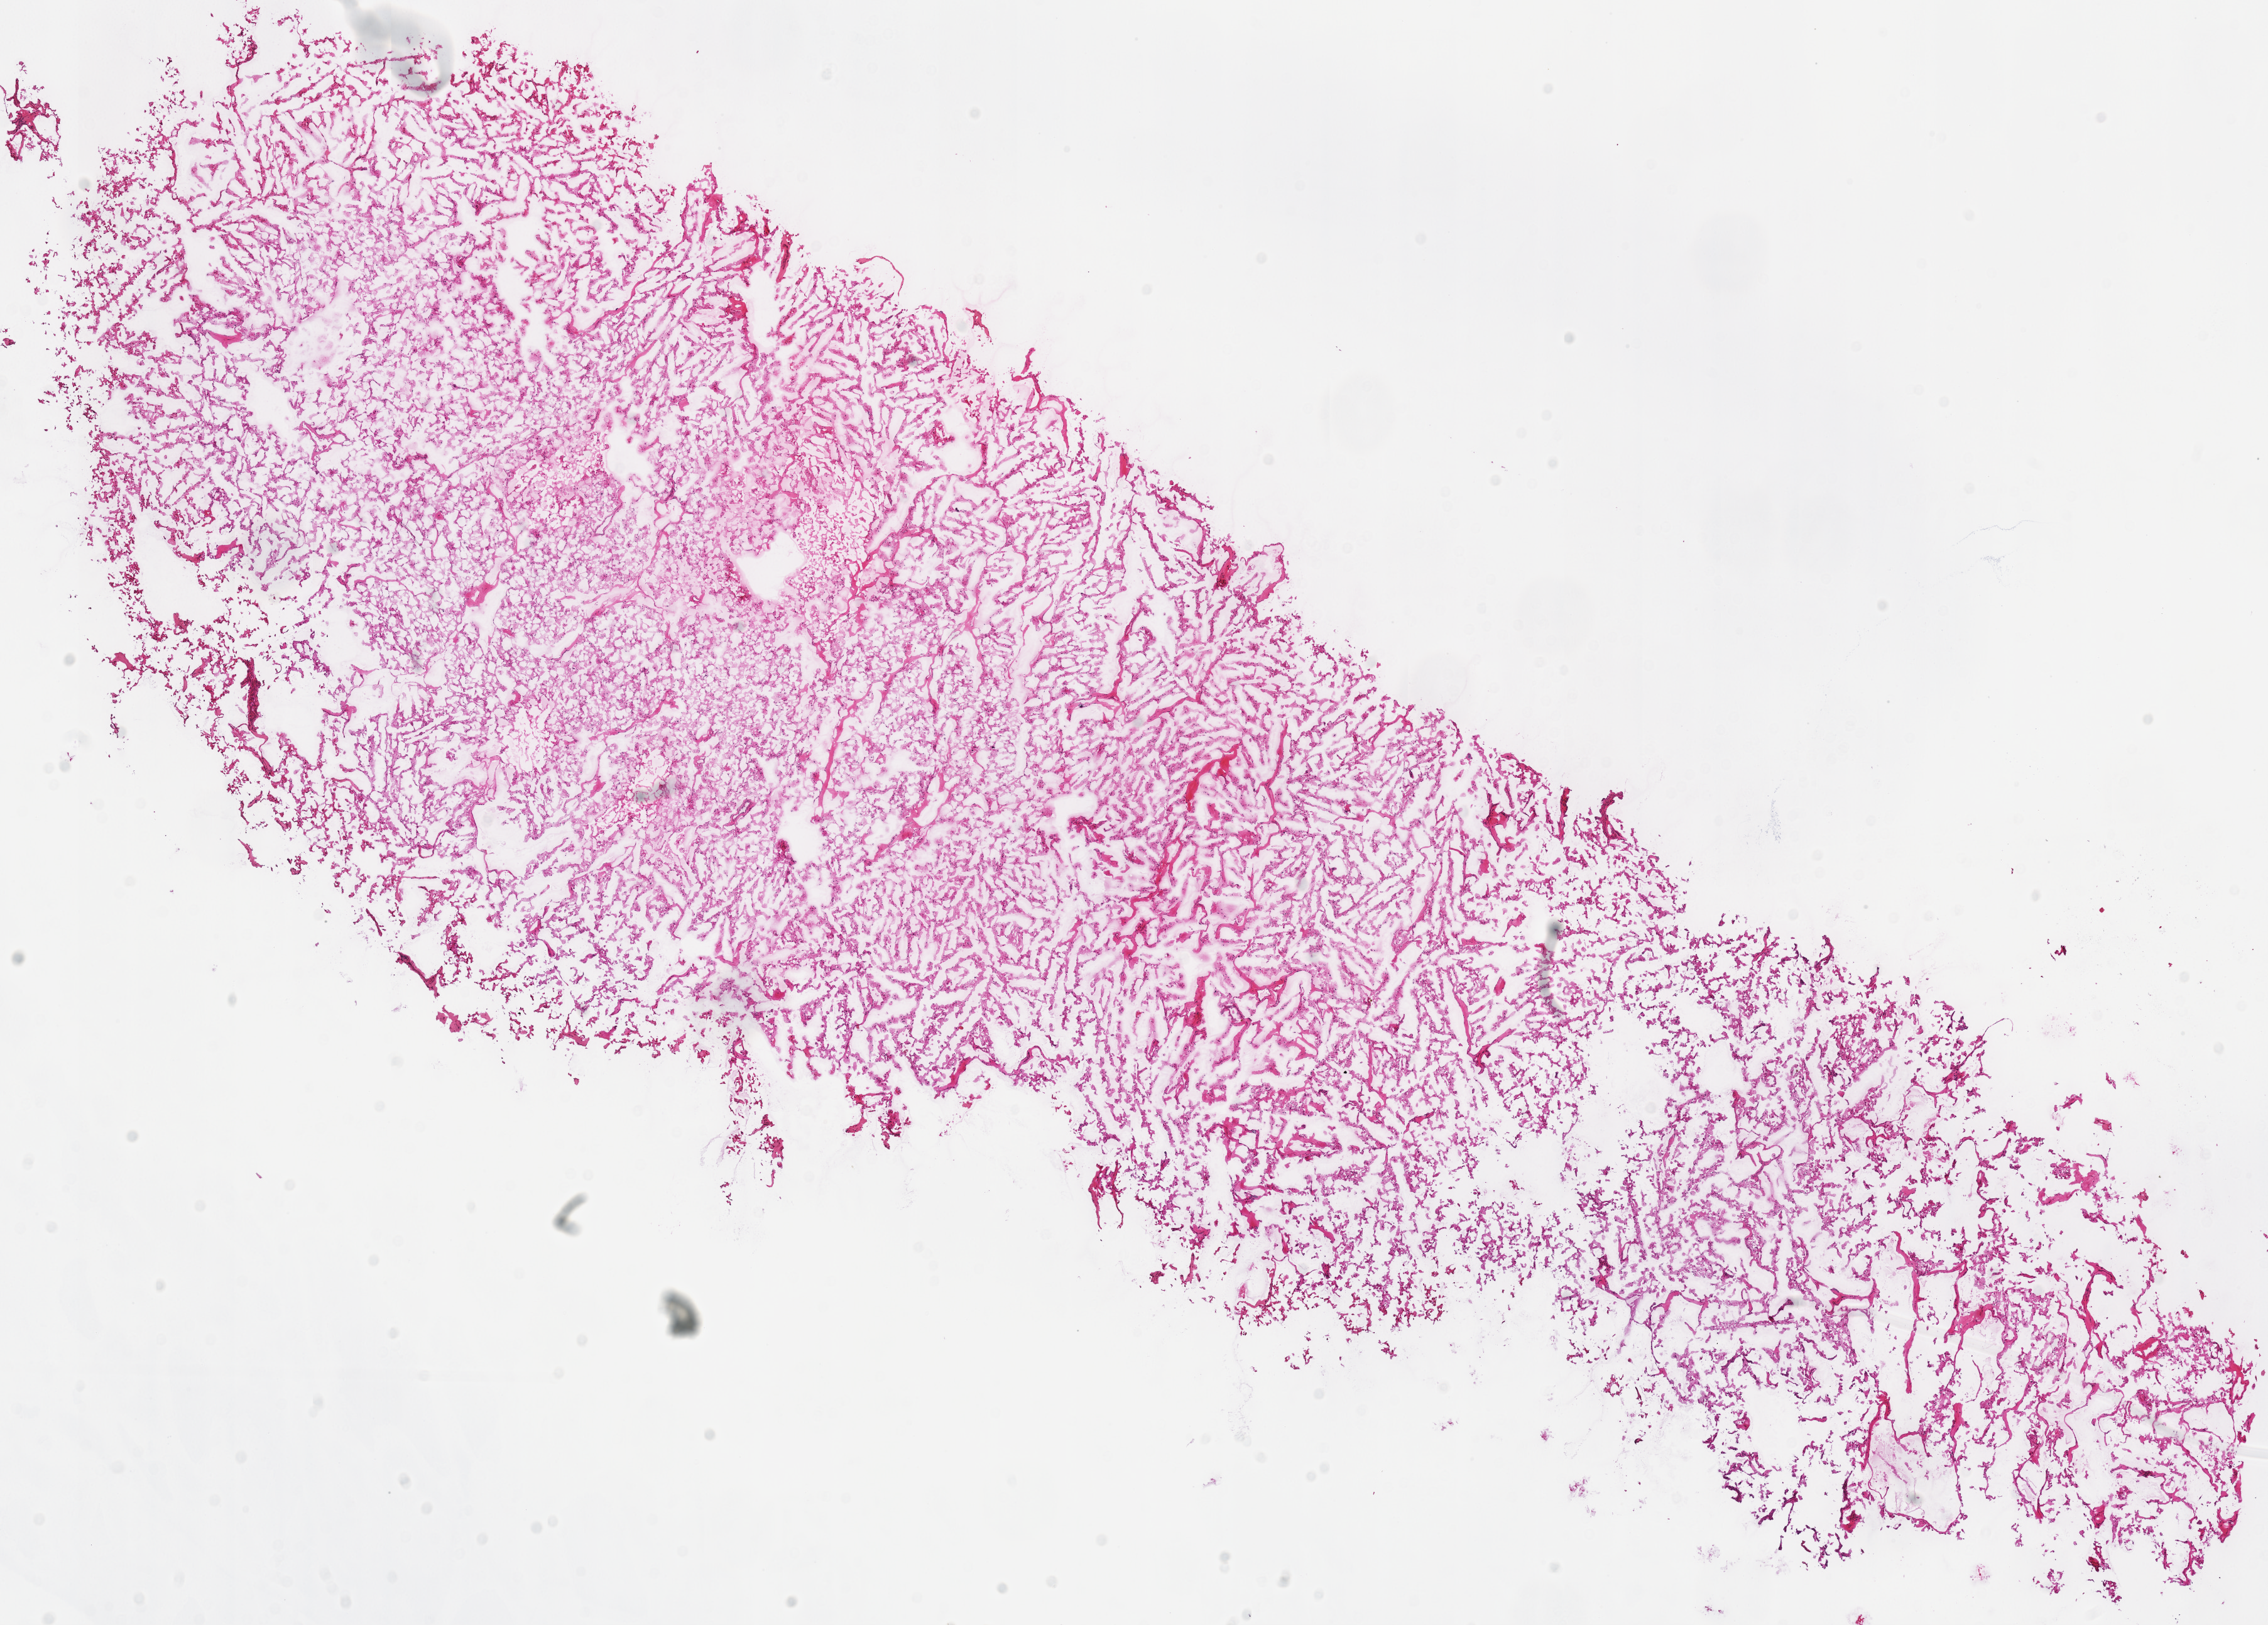
H&E whole-slide image, whole scanned area (about 14.2 x 10.2 mm, from a 40x scan) shown as a low-resolution overview; frozen section from the top of the tissue portion; kidney, primary tumour sample. Patient: male, age at initial diagnosis 49 years. Slide review estimates, as recorded: tumour cells 90%, tumour nuclei 85%, normal cells 0%, stromal cells 10%, necrosis 0%.
AJCC pathologic stage: I. Diagnosis: Renal cell carcinoma, chromophobe type.